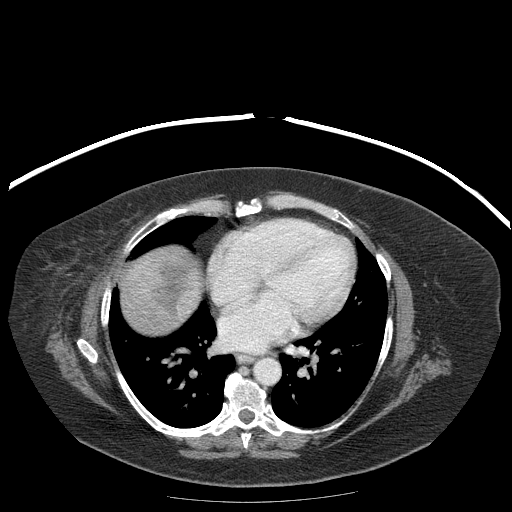
Contrast-enhanced abdominal CT (liver protocol), one axial slice; position 183 of 204 along the scan axis; reconstruction kernel STANDARD; 120 kVp; soft-tissue window (W 400 / L 40 HU); 2.5 mm slice thickness; 512 × 512 image matrix, field of view 440 × 440 mm. From the clinical record (not read from this slice): diagnosis: hepatocellular carcinoma (patient treated with transarterial chemoembolisation; whether this scan precedes or follows treatment is not stated here); TNM stage (as recorded): Stage-IIIB; Child-Pugh class: A; tumour differentiation: well differentiated; tumour nodularity: uninodular.
Outlined on this slice (semi-automatic segmentation, software-assisted and operator-edited):
- liver parenchyma outside the tumour (the mass and vessels are separate outlines, so this box may not span the whole liver): bounding box <120,246,200,334> (left, top, right, bottom; pixels)
- mass: <136,251,200,318>